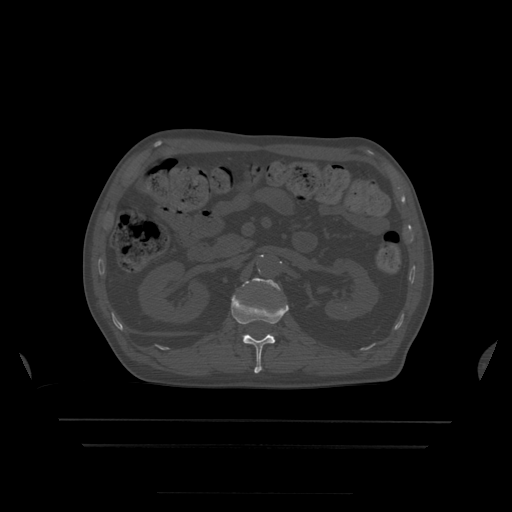
CT including the spine, one axial slice. Position 165 of 522 along the scan axis. Bone window (W 1800 / L 400 HU). 1.25 mm slice thickness. 512 × 512 image matrix, field of view 436 × 436 mm. Patient age 68 years. Case-level facts recorded for this patient, not image findings: primary cancer: urothelial.
Annotated regions visible in this slice (semi-automatic segmentation, software-assisted and operator-edited):
- L1 vertebra: bounding box [x1, y1, x2, y2] px = [231, 289, 289, 374]
- L2 vertebra: [243, 278, 281, 290]